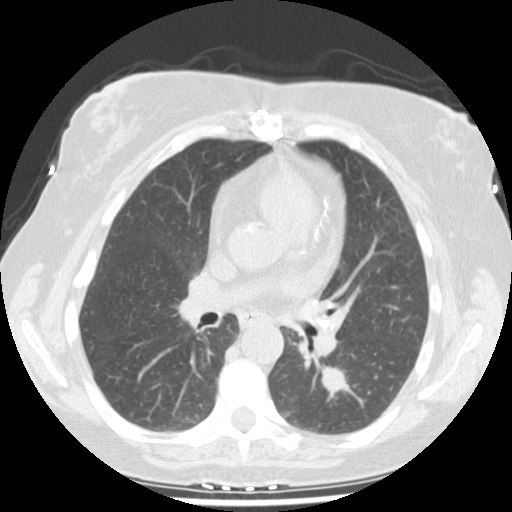
Low-dose screening chest CT, one axial slice; slice 95 of 159 in the series (ordered by position); reconstruction kernel STANDARD; 120 kVp; lung window (W 1500 / L -600 HU); 2.5 mm slice thickness; 512 × 512 image matrix.
Outlined on this slice (outlined manually by an expert reader):
- lesion 1 (tumor, lower lobe of left lung): bounding box (x1, y1, x2, y2) in pixels: (320, 366, 348, 394)